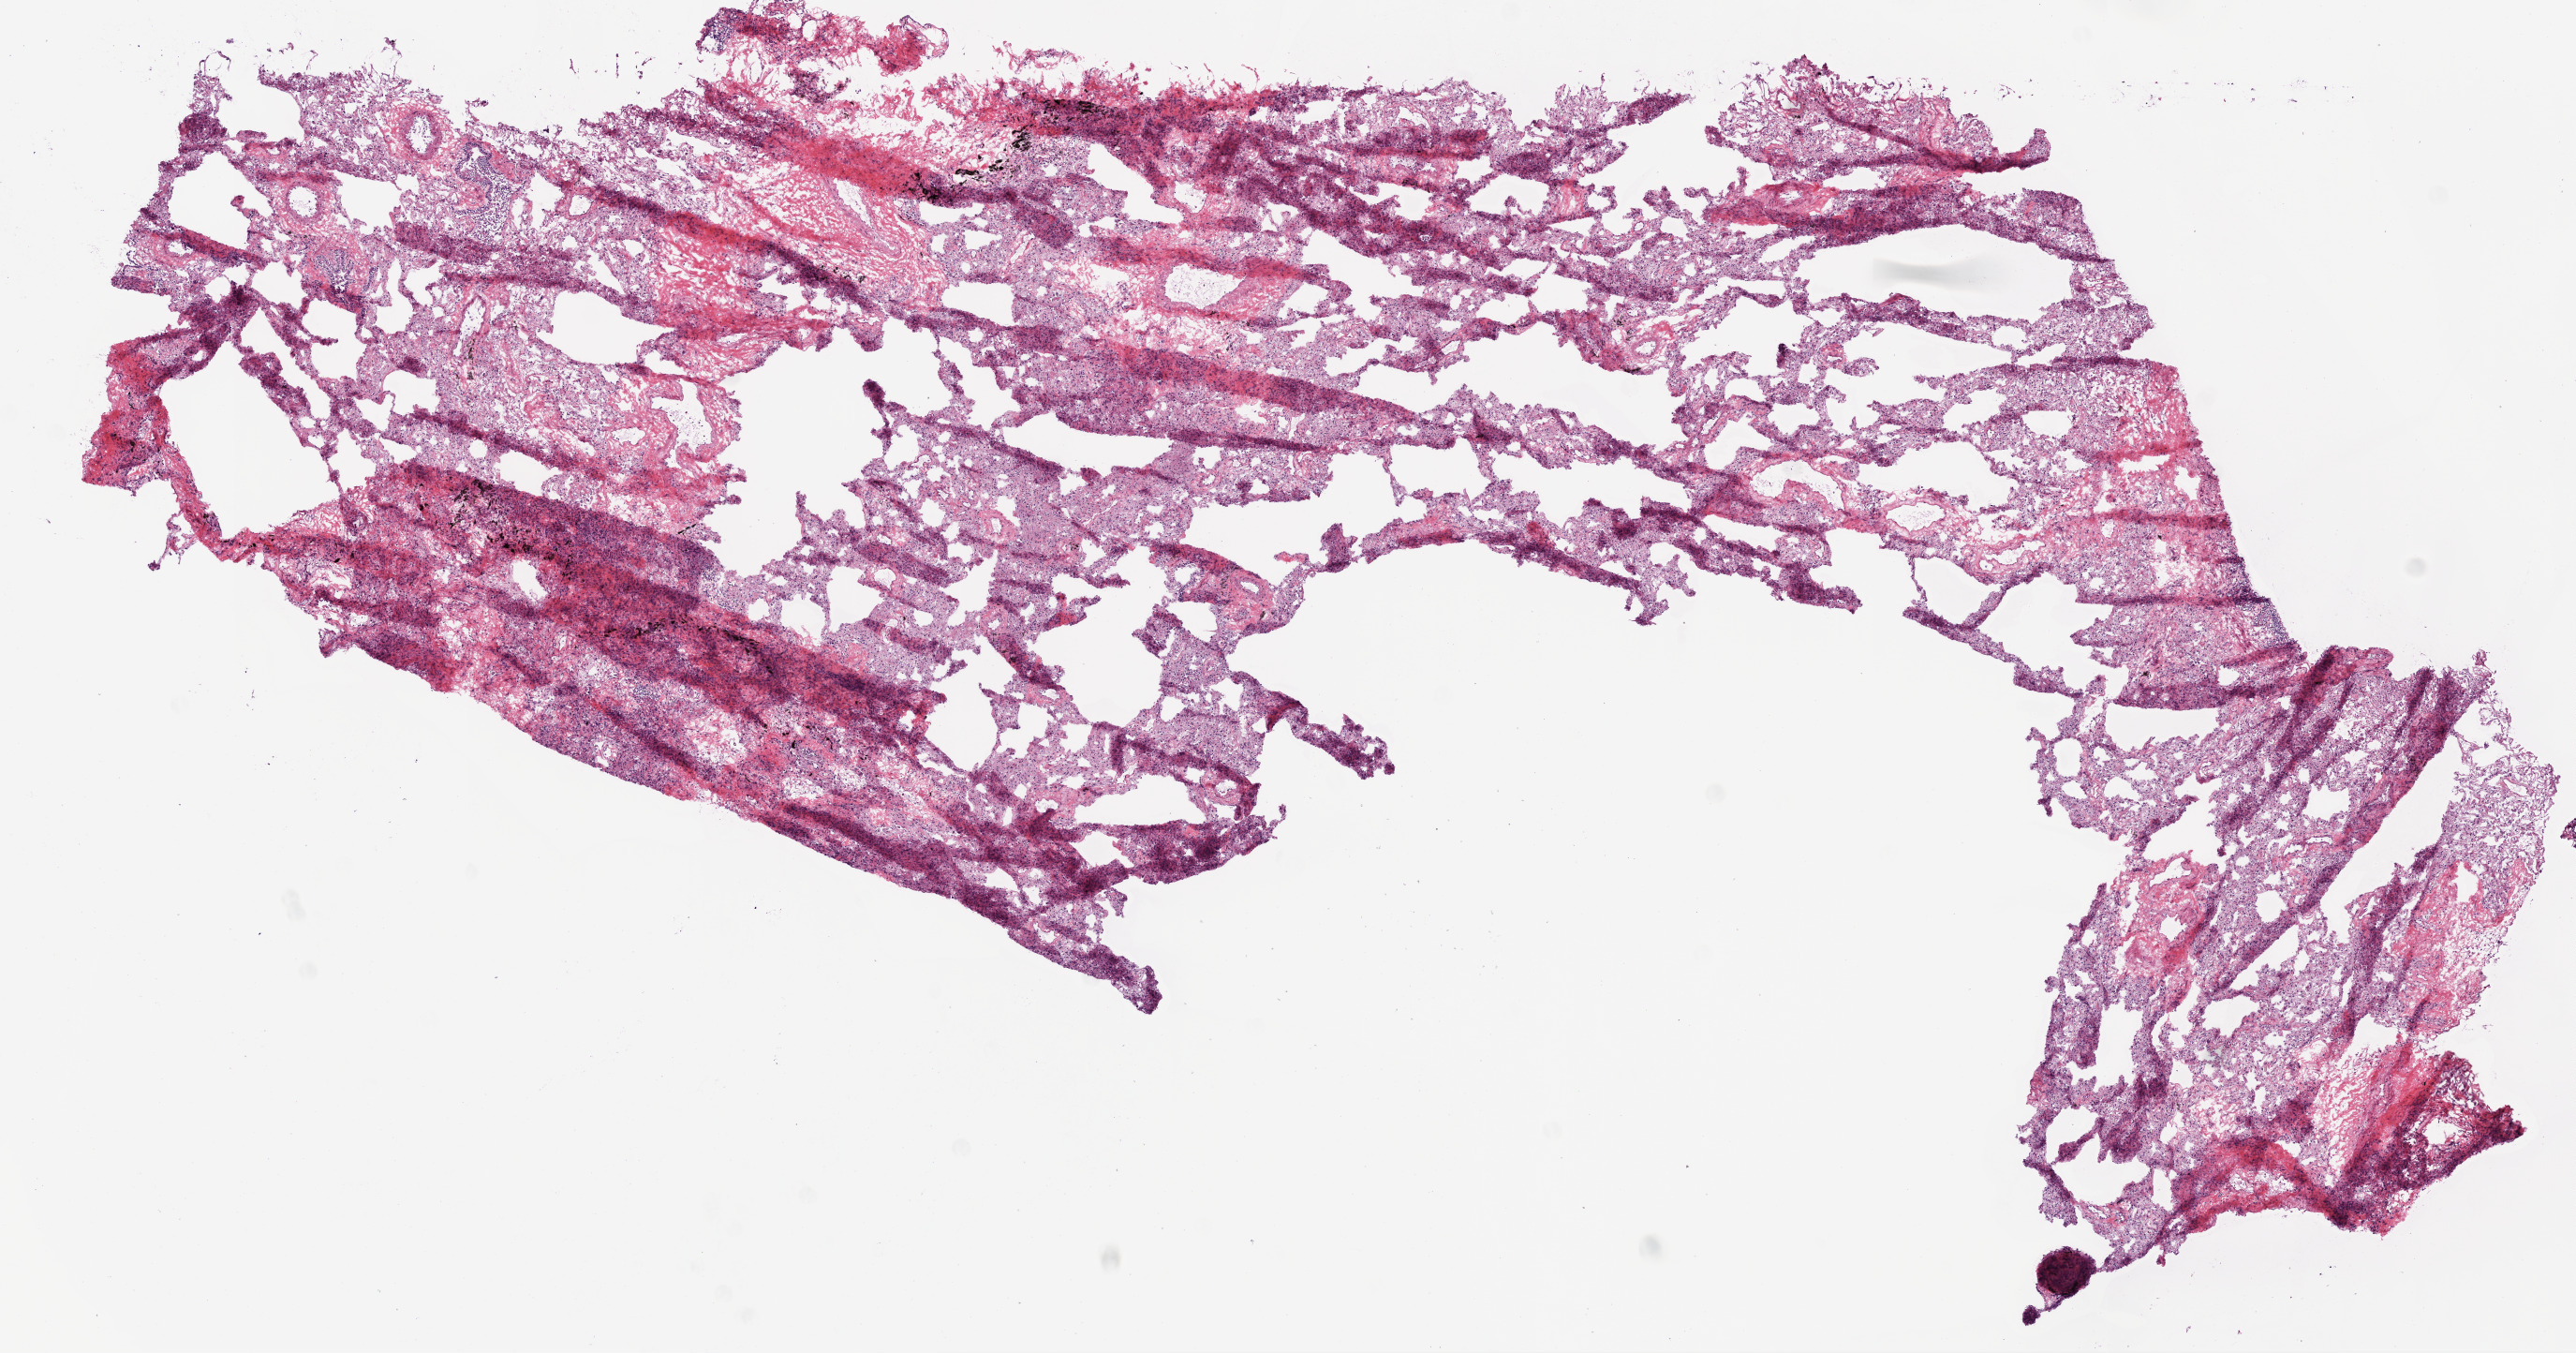
H&E-stained whole-slide image — a low-resolution overview of the entire scanned area, about 11.0 x 5.8 mm (from a 20x scan), frozen section, lung, solid tissue normal (non-tumour tissue) sample. Patient: male, age at initial diagnosis 70 years.
This section: solid tissue normal sample (biorepository sample class). Patient diagnosis: Squamous cell carcinoma, NOS (upper lobe, lung).